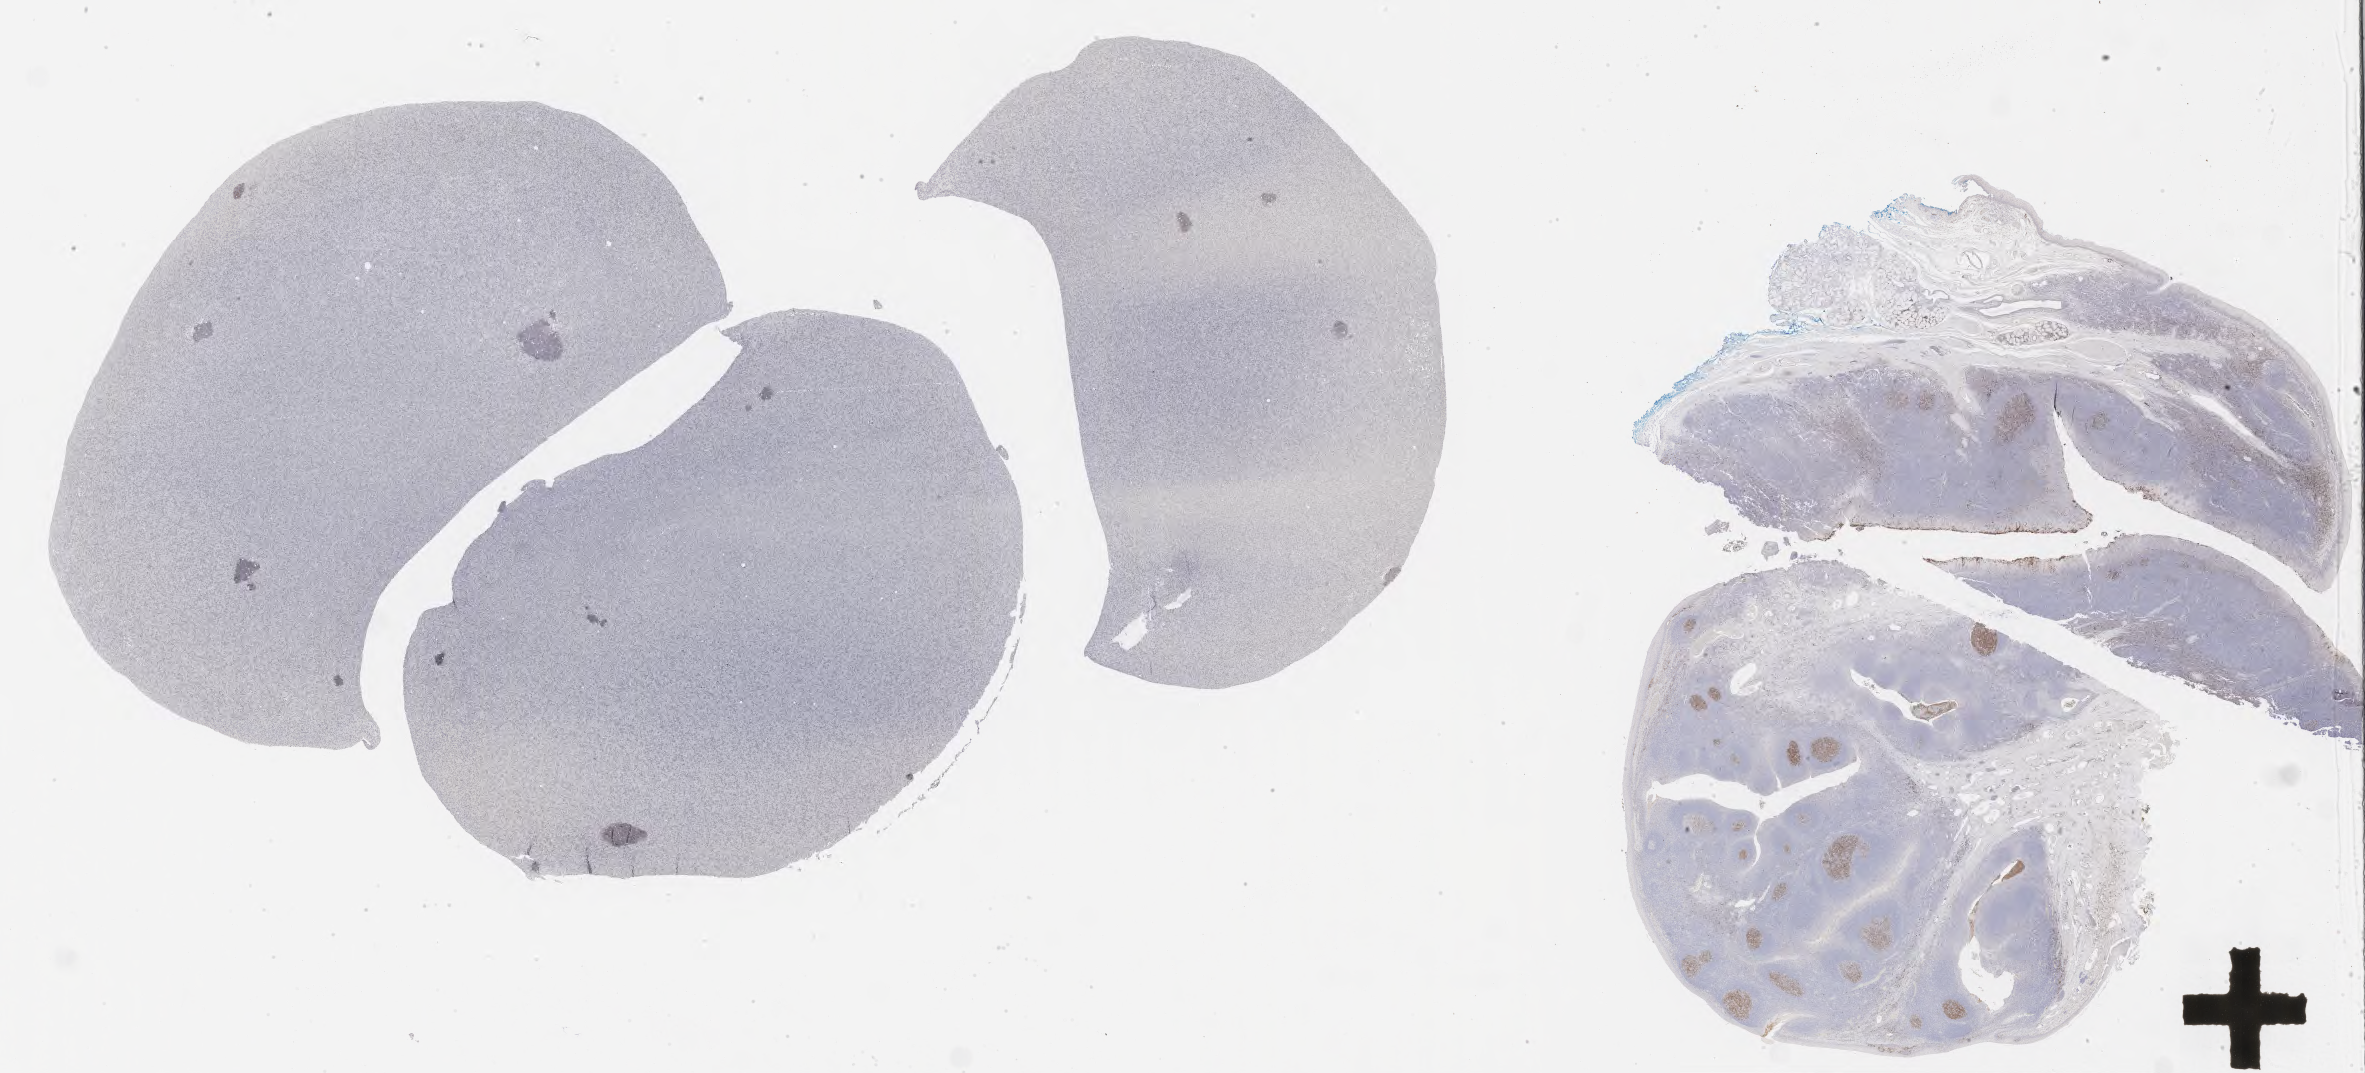
Whole-slide image, immunohistochemical stain for CD10, a low-resolution overview of the entire scanned area, about 38.2 x 17.4 mm. Specimen: tumor tissue. Male patient, age 17 years.
Histologic diagnosis: Burkitt lymphoma, NOS.